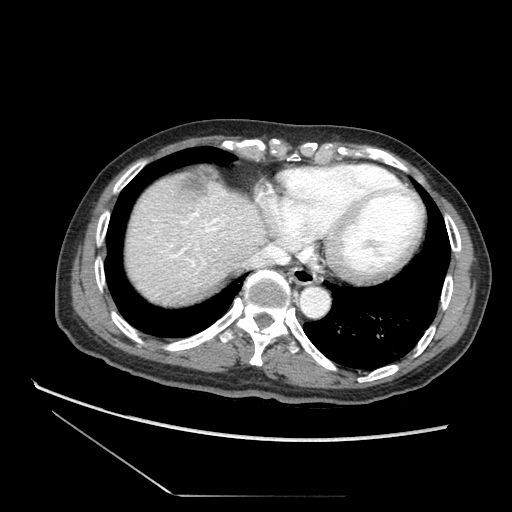
Contrast-enhanced abdominal CT (liver protocol), one axial slice. Position 68 of 73 along the scan axis. Soft-tissue window (W 400 / L 40 HU). 512 × 512 image matrix, field of view 360 × 360 mm. Case-level facts recorded for this patient, not image findings: diagnosis: hepatocellular carcinoma (patient treated with transarterial chemoembolisation; whether this scan precedes or follows treatment is not stated here); TNM stage (as recorded): Stage-II; Child-Pugh class: A; tumour differentiation: moderately differentiated; tumour nodularity: multinodular.
Annotated regions visible in this slice (semi-automatic segmentation, software-assisted and operator-edited):
- abdominal aorta: box from (x=302, y=287) to (x=330, y=317) px
- liver parenchyma outside the tumour (the mass and vessels are separate outlines, so this box may not span the whole liver): (x=118, y=172)–(x=274, y=312)
- mass: (x=131, y=275)–(x=142, y=284)
- liver vessels: (x=193, y=244)–(x=205, y=261)